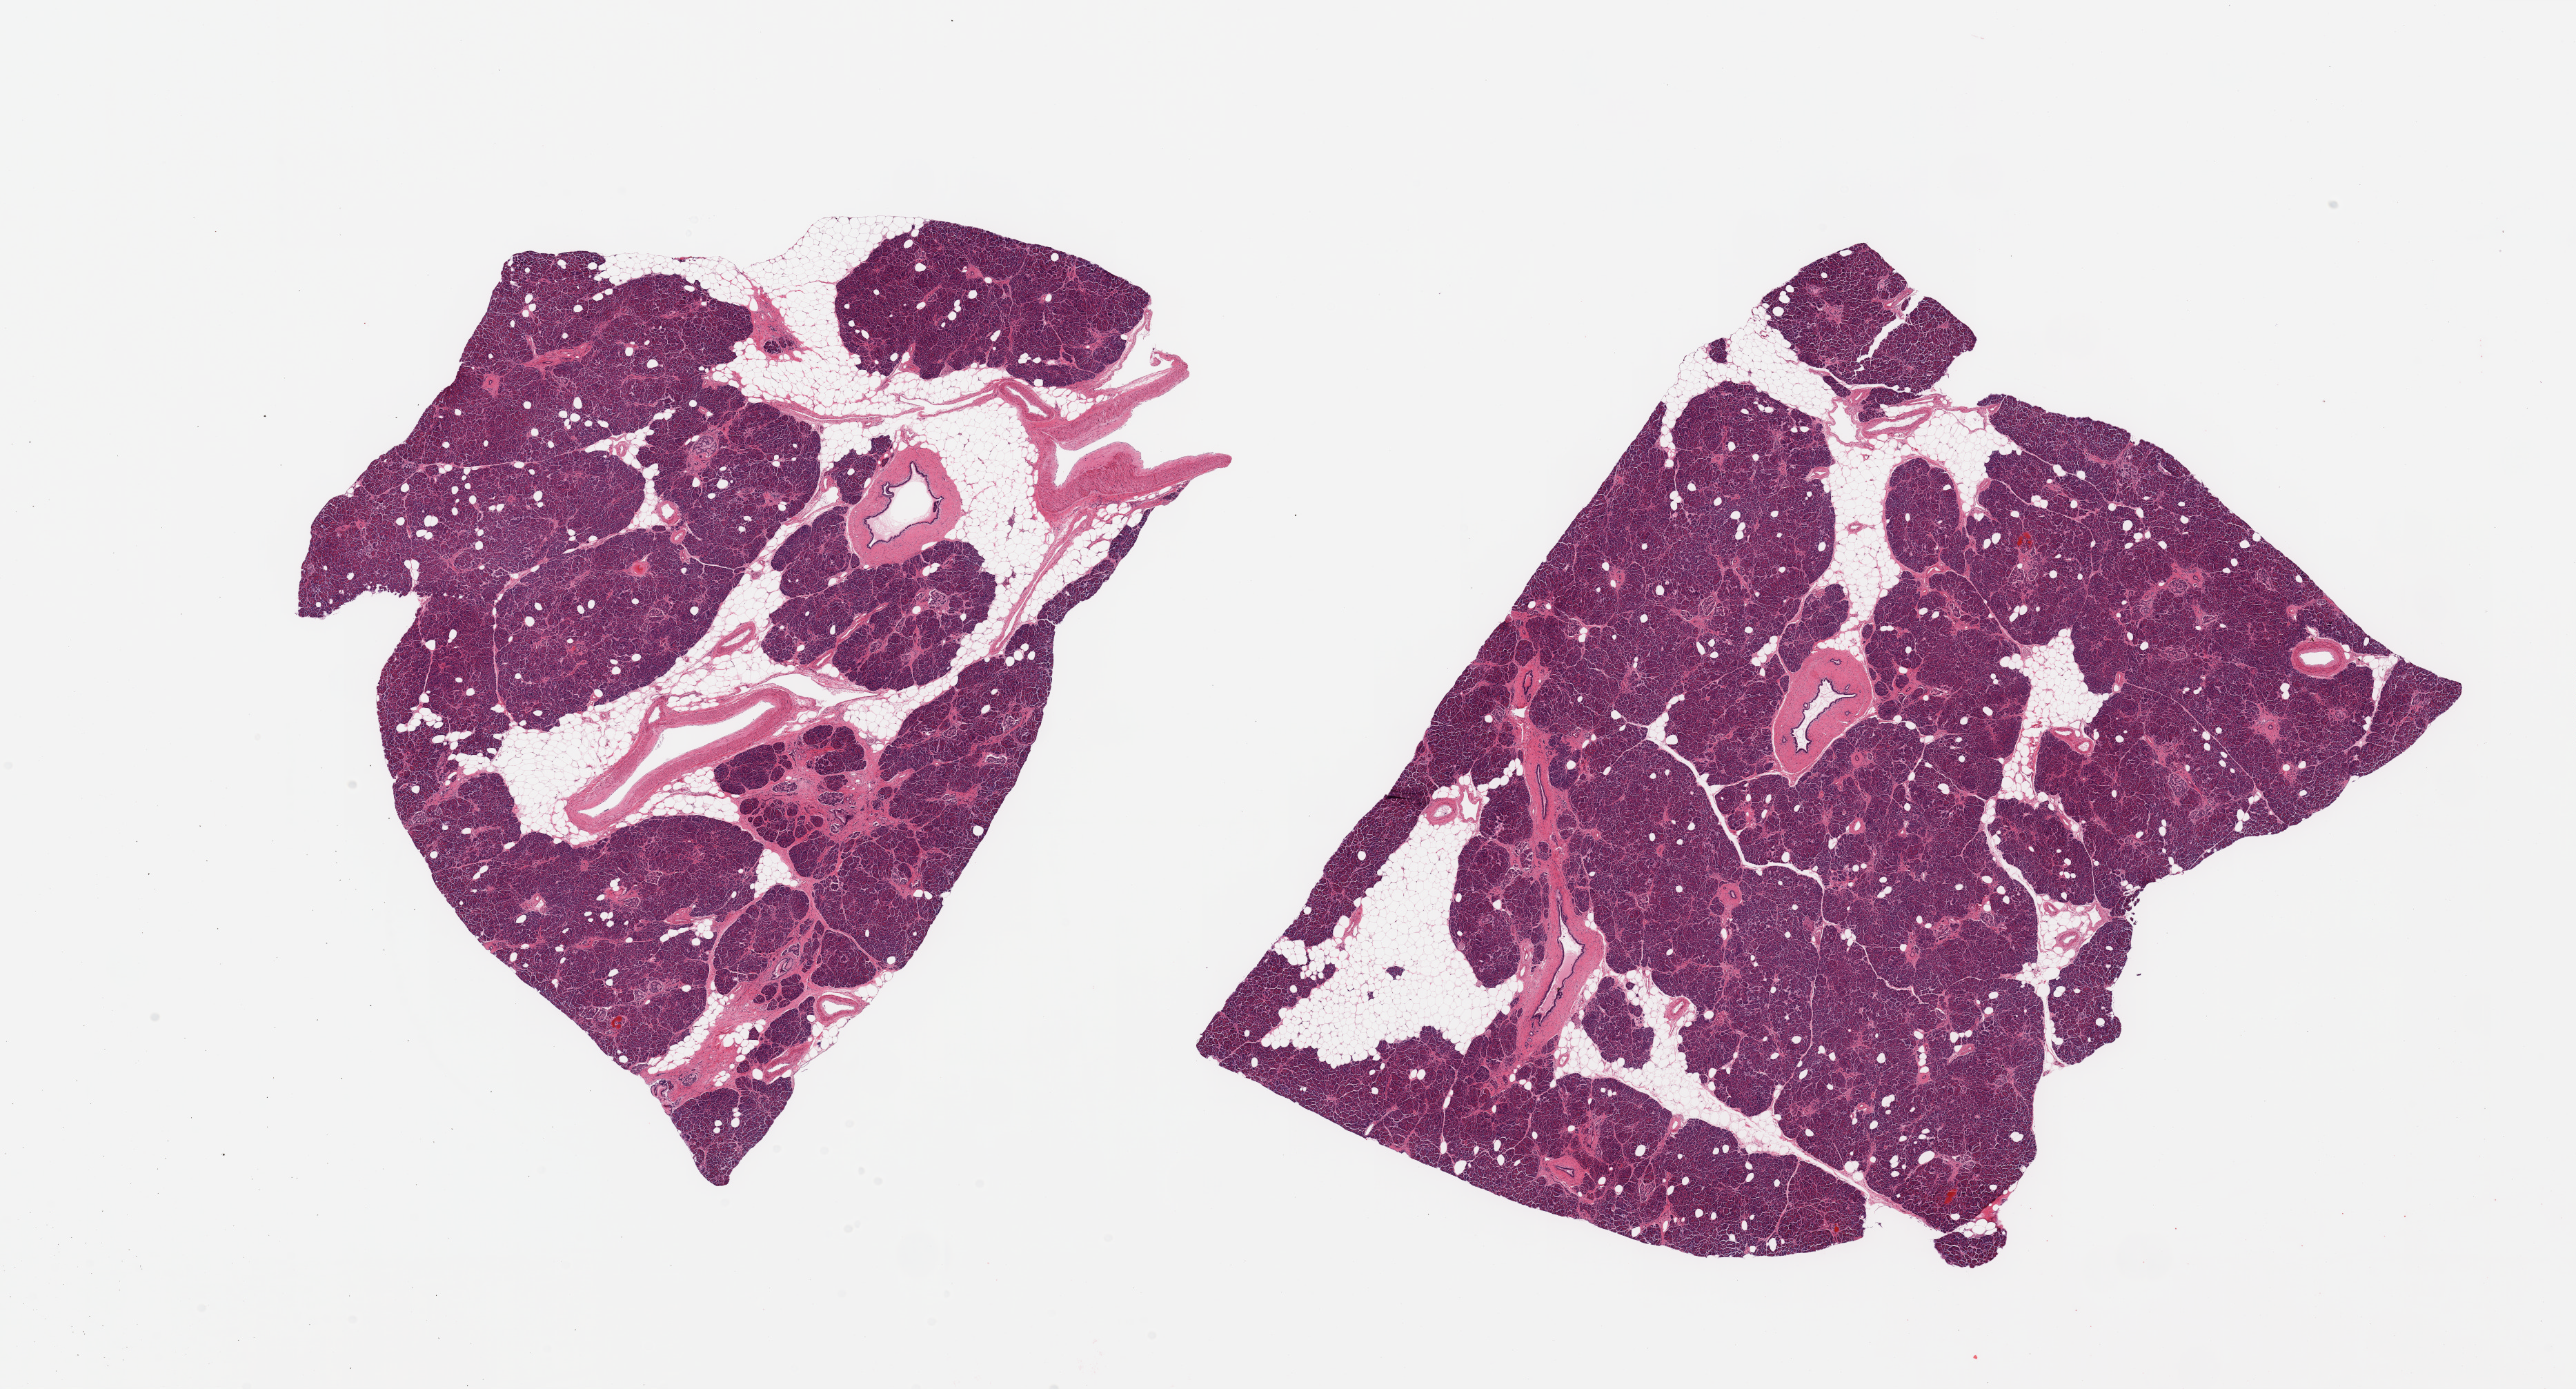
Whole-slide image, H&E stain — a low-resolution overview of the entire scanned area, about 29.5 x 15.9 mm (slide scanned at 20x). PAXgene-fixed, paraffin-embedded tissue. Section of pancreas (target tissue). Tissue donor sample.
• pathologist's review note for this sample: 2 pieces, evidence of remote pancreatitis; Islets well visualized though not numerous